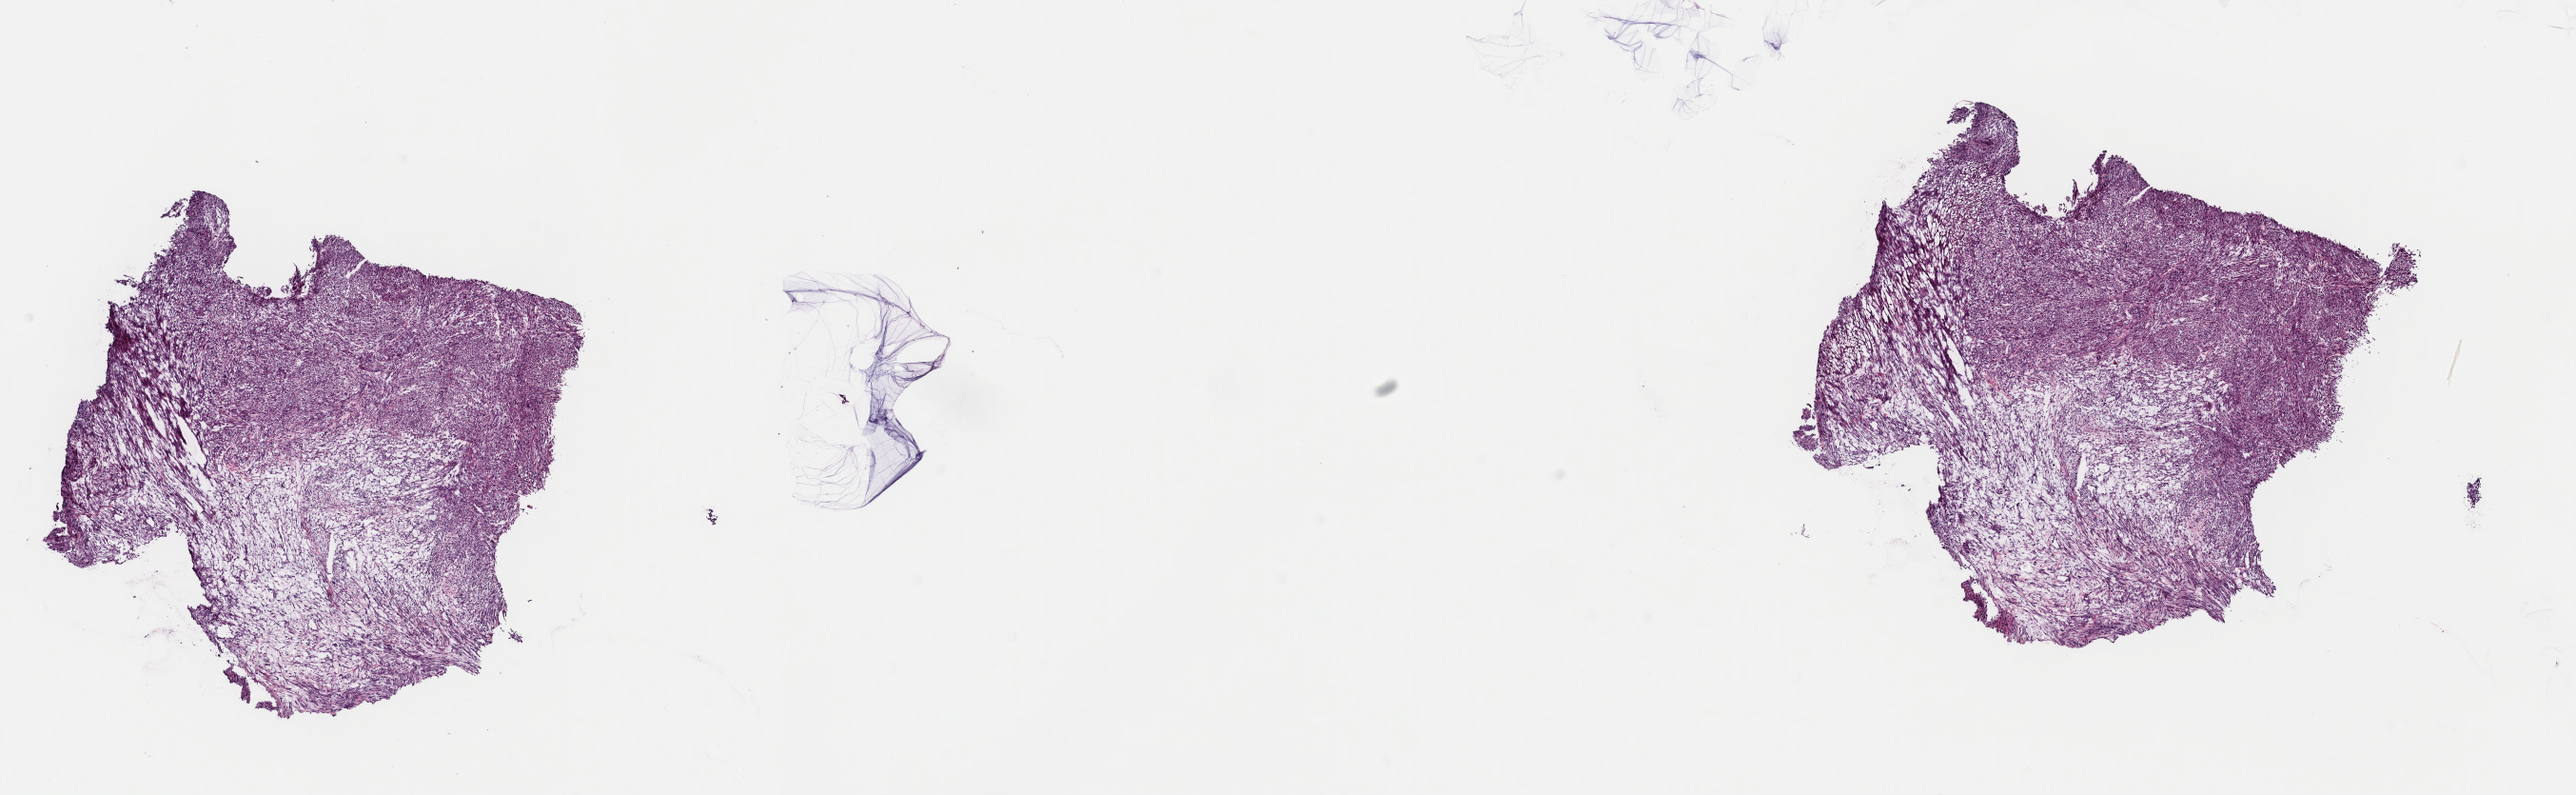
Digitized H&E-stained tissue section (whole slide), whole scanned area (about 21.4 x 6.6 mm, from a 40x scan) shown as a low-resolution overview; frozen section; primary tumour sample from the connective, subcutaneous and other soft tissues. Male, age 67 years at initial diagnosis. Pathologist review of this section (percent, as recorded): tumour cells 100%, tumour nuclei 88%, normal cells 0%, stromal cells 0%, necrosis 0%. Inflammatory infiltration, as recorded: lymphocyte infiltration 0%, monocyte infiltration 0%, neutrophil infiltration 0%.
Histologic diagnosis: Leiomyosarcoma, NOS (connective, subcutaneous and other soft tissues of lower limb and hip).